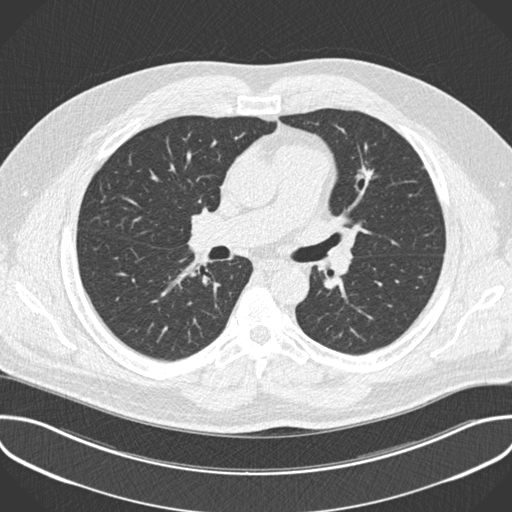
Axial slice from a low-dose chest CT screening exam; baseline screening round; lung window (W 1500 / L -600 HU); 2 mm slice thickness; standard (soft-tissue) reconstruction kernel (B30f); 512 × 512 image matrix. Male participant, aged 55 years at enrolment. Former smoker at enrolment.
Expert-annotated lung lesion, bounding box (x1, y1, x2, y2) in pixels: (343, 158, 392, 193). The exam's reader record, not a measurement of the box and not confirmed to be the same lesion: non-calcified nodule or mass ≥4 mm, lingula, 13 × 12 mm, spiculated (stellate) margins, soft tissue attenuation. Official screen result: positive, change unspecified: nodule(s) >= 4 mm or enlarging nodule(s), mass(es), or other non-specific abnormalities suspicious for lung cancer. Participant outcome: lung cancer diagnosed 169 days after this screen — adenocarcinoma, NOS, left upper lobe, stage IA (AJCC 6th edition), 13 mm at pathology.